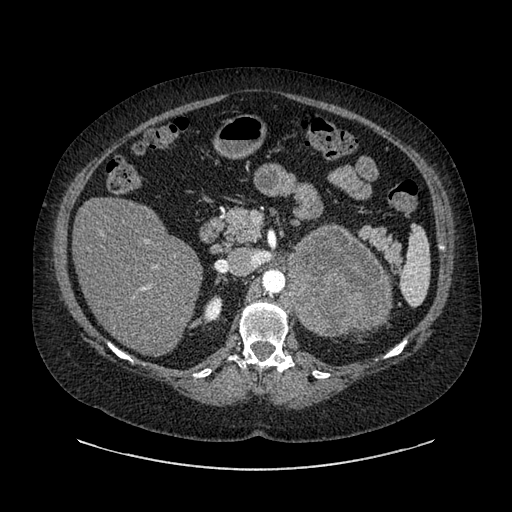
Contrast-enhanced abdominal CT, one axial slice. Position 554 of 769 along the scan axis. Reconstruction kernel SOFT. 120 kVp. Intravenous contrast given. Soft-tissue window (W 400 / L 40 HU). 0.62 mm slice thickness. 512 × 512 image matrix, field of view 460 × 460 mm. Female patient, age 61 years. From the clinical record (not read from this slice): diagnosis: adrenocortical carcinoma; tumour side: left adrenal; tumour size at pathology: 13 cm; Ki-67 index: 79 %; stage (as recorded): 2.
Outlined on this slice (semi-automatic segmentation, software-assisted and operator-edited):
- mass: box from (x=289, y=228) to (x=388, y=336) px